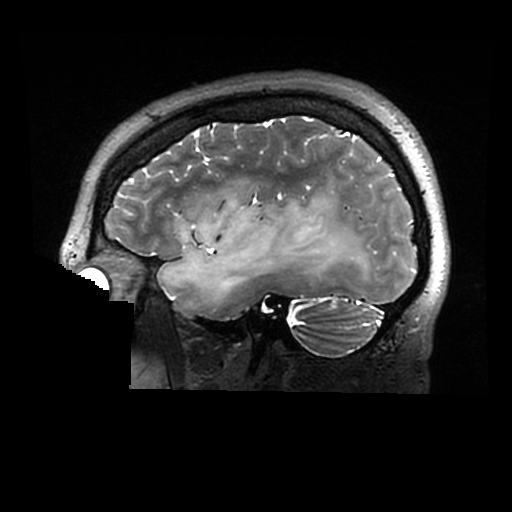
Brain MRI from a brain-tumour surgery series, one sagittal slice. Position 220 of 320 along the scan axis. 0.6 mm slice thickness. 512 × 512 image matrix, field of view 240 × 240 mm. Case-level facts recorded for this patient, not image findings: histopathology: Astrocytoma; WHO grade: 2; IDH mutation: yes.
Annotated regions visible in this slice (outlined manually by an expert reader):
- tumour: box from (x=158, y=191) to (x=378, y=309) px